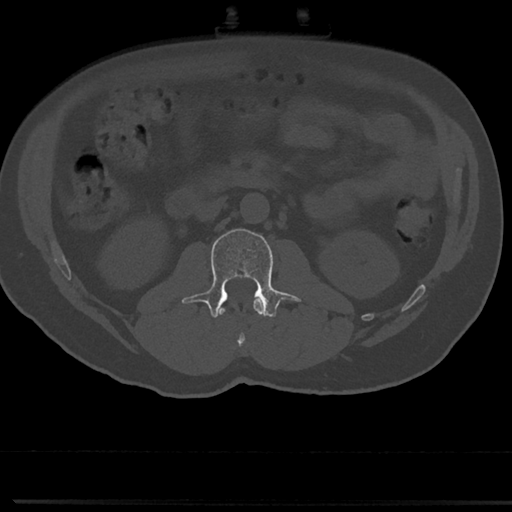
CT including the spine, one axial slice. Position 27 of 817 along the scan axis. Reconstruction kernel Br40s/3. 120 kVp. Bone window (W 1800 / L 400 HU). 0.5 mm slice thickness. 512 × 512 image matrix. Patient: male, 61 years. Case-level facts recorded for this patient, not image findings: primary cancer: prostate.
Outlined on this slice (semi-automatic segmentation, software-assisted and operator-edited):
- L1 vertebra: box from (x=219, y=298) to (x=263, y=350) px
- L2 vertebra: (x=191, y=228)–(x=297, y=319)